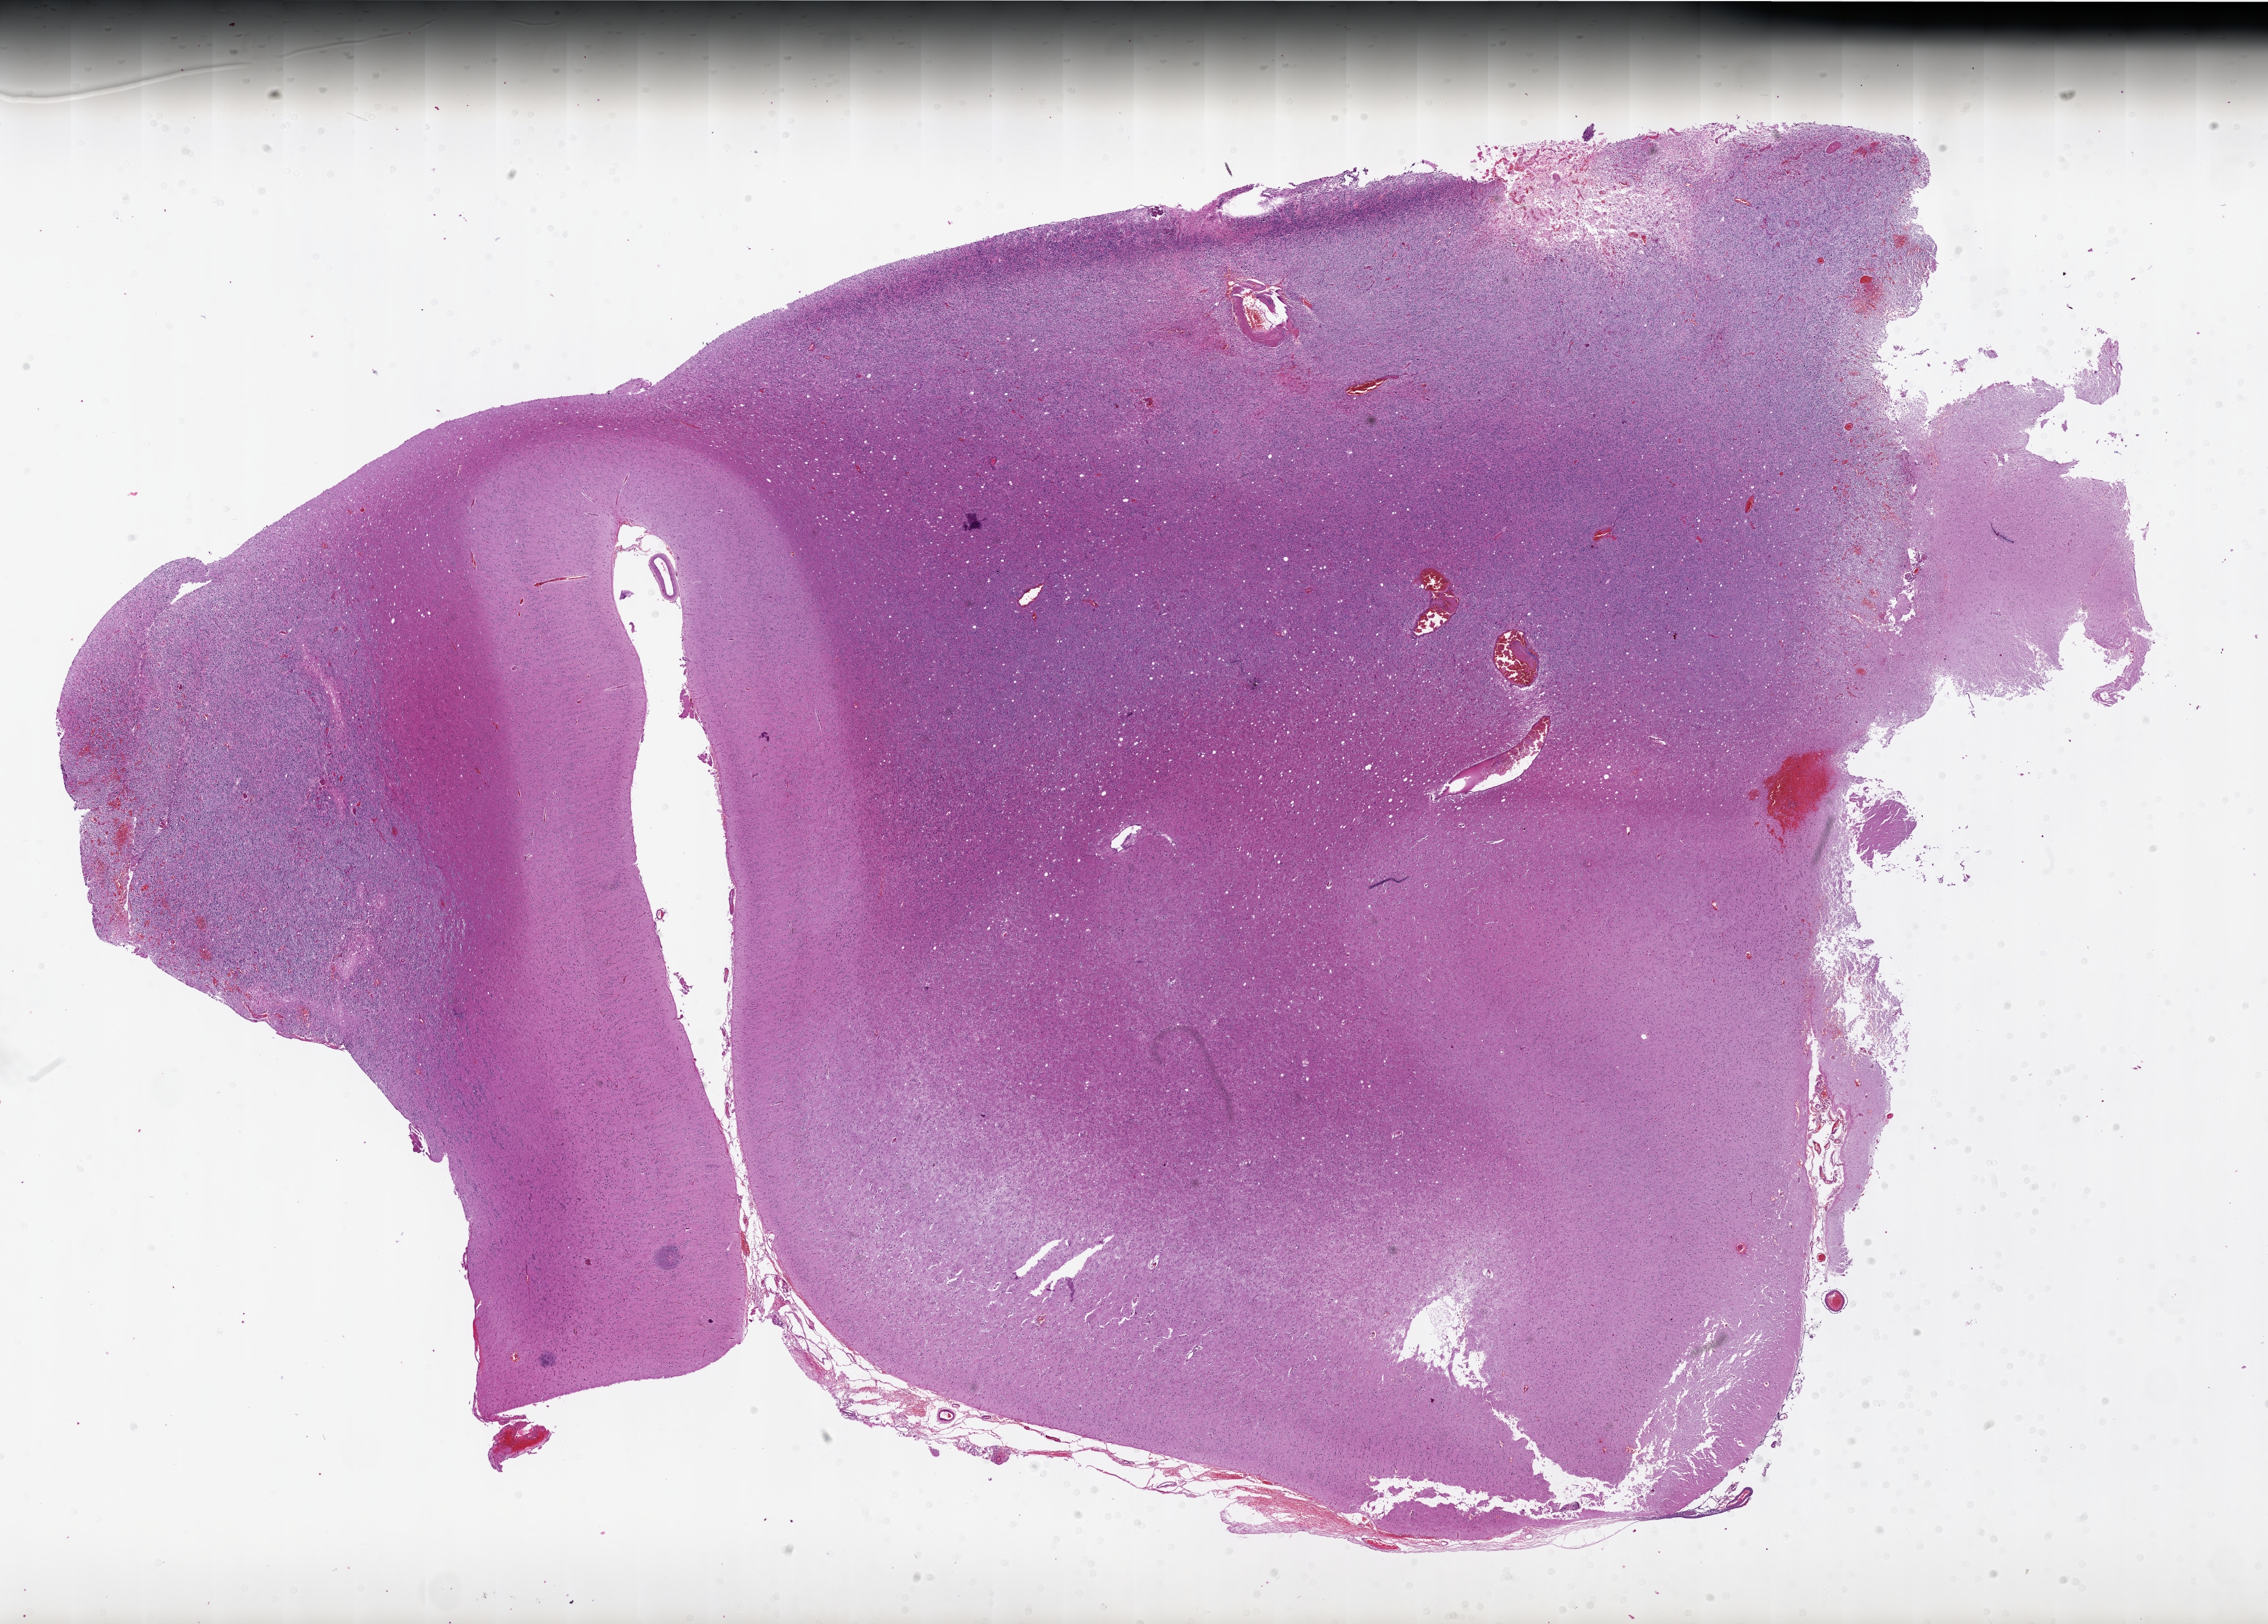
Whole-slide histology image, Hematoxylin and eosin (H&E) stained — low-resolution overview of the scanned area, about 32.0 x 22.9 mm (slide scanned at 20x), formalin-fixed paraffin-embedded (FFPE) diagnostic section, brain, primary tumour sample. Patient: male, age at initial diagnosis 49 years.
Pathologic diagnosis: Glioblastoma.